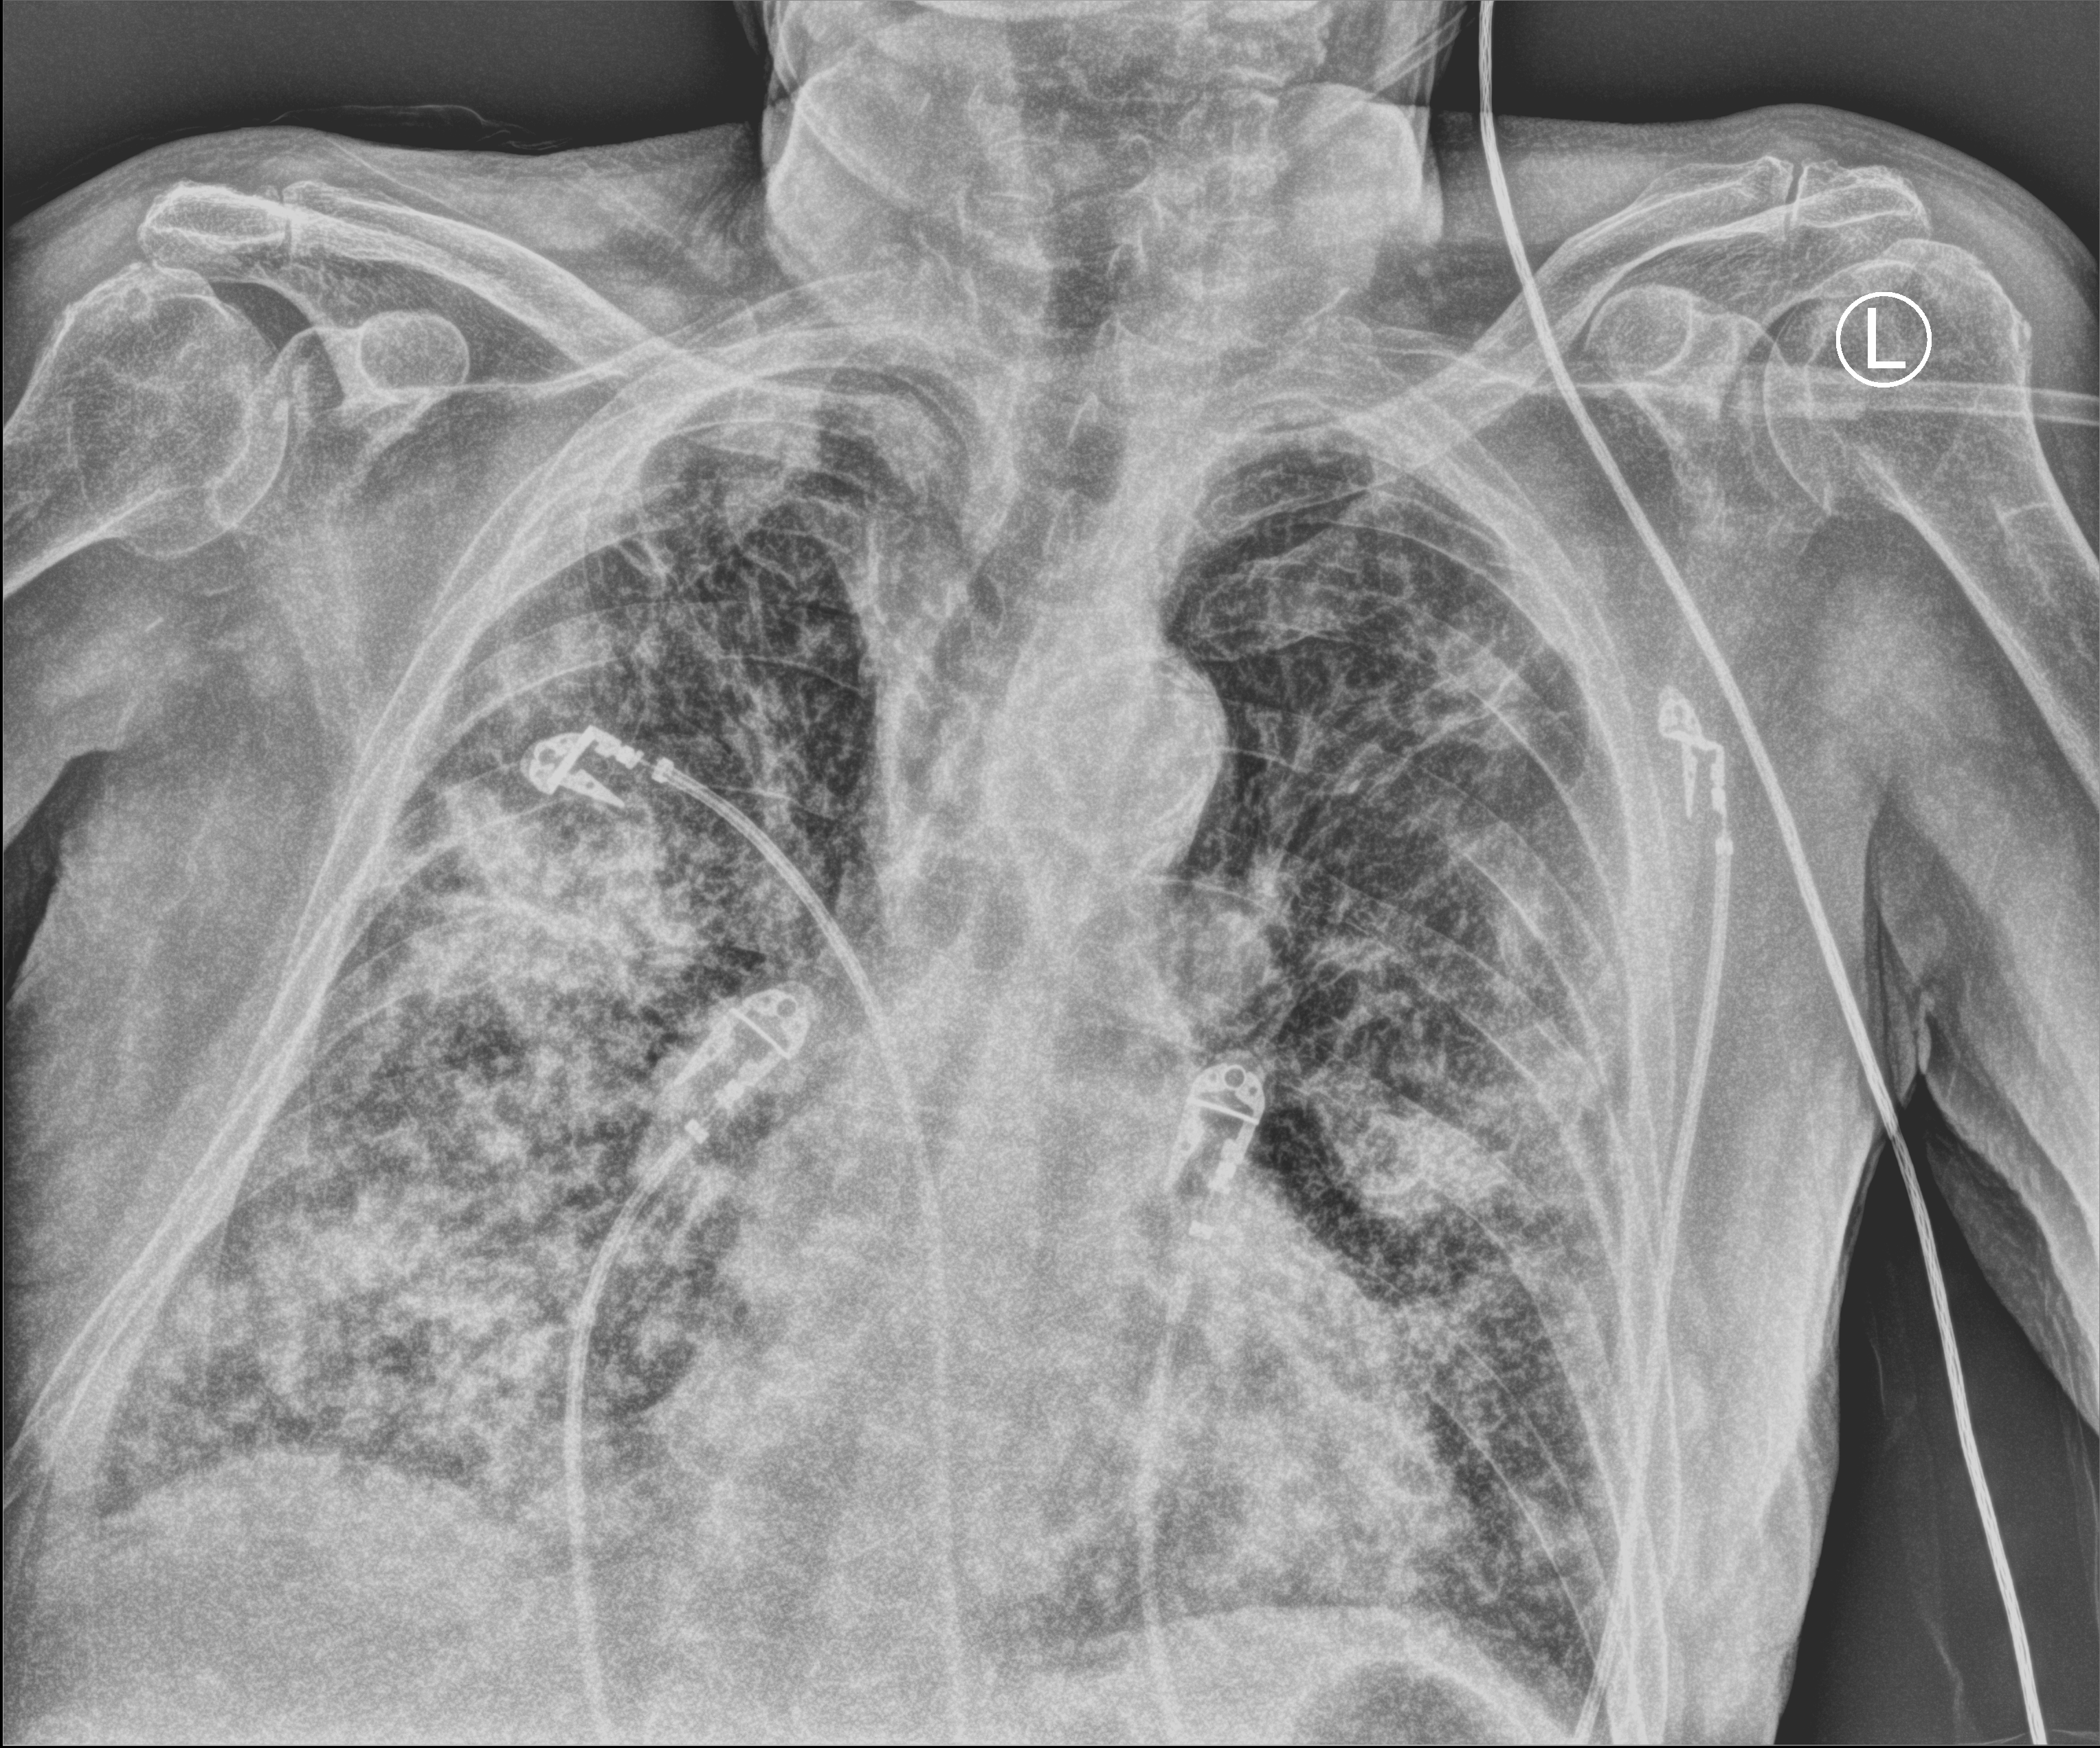
Bedside chest radiograph (computed radiography); anteroposterior (AP) projection. Patient hospitalised with COVID-19; male, aged 75–90 years.
From the hospital-stay record, not from the radiograph (when in the stay this image was taken is not recorded): mechanically ventilated during this hospital stay: no; admitted to intensive care during this hospital stay: no.